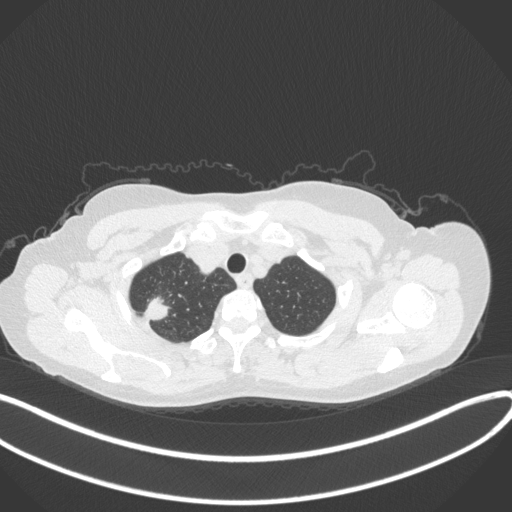
Chest CT, one axial slice. Slice 321 of 342 in the series (ordered by position). Reconstruction kernel B31f. 120 kVp. Lung window (W 1500 / L -600 HU). 512 × 512 image matrix, field of view 400 × 400 mm. Patient: female, 50 years. From the clinical record (not read from this slice): clinical TNM (as recorded): T1c N0 M0; histopathological grade: G2-3.
Annotated regions visible in this slice (rectangle marked by the reading radiologist):
- lung tumour (recorded histology: adenocarcinoma): bounding box (x1, y1, x2, y2) in pixels: (144, 296, 170, 320)